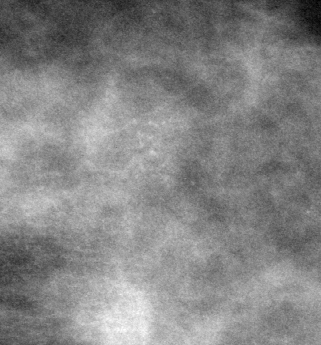
Cropped region of a digitized screen-film mammogram centred on a radiologist-marked abnormality, left breast, CC view.
- Calcifications, morphology amorphous, distribution clustered; BI-RADS assessment category 4; pathology (as recorded): benign.